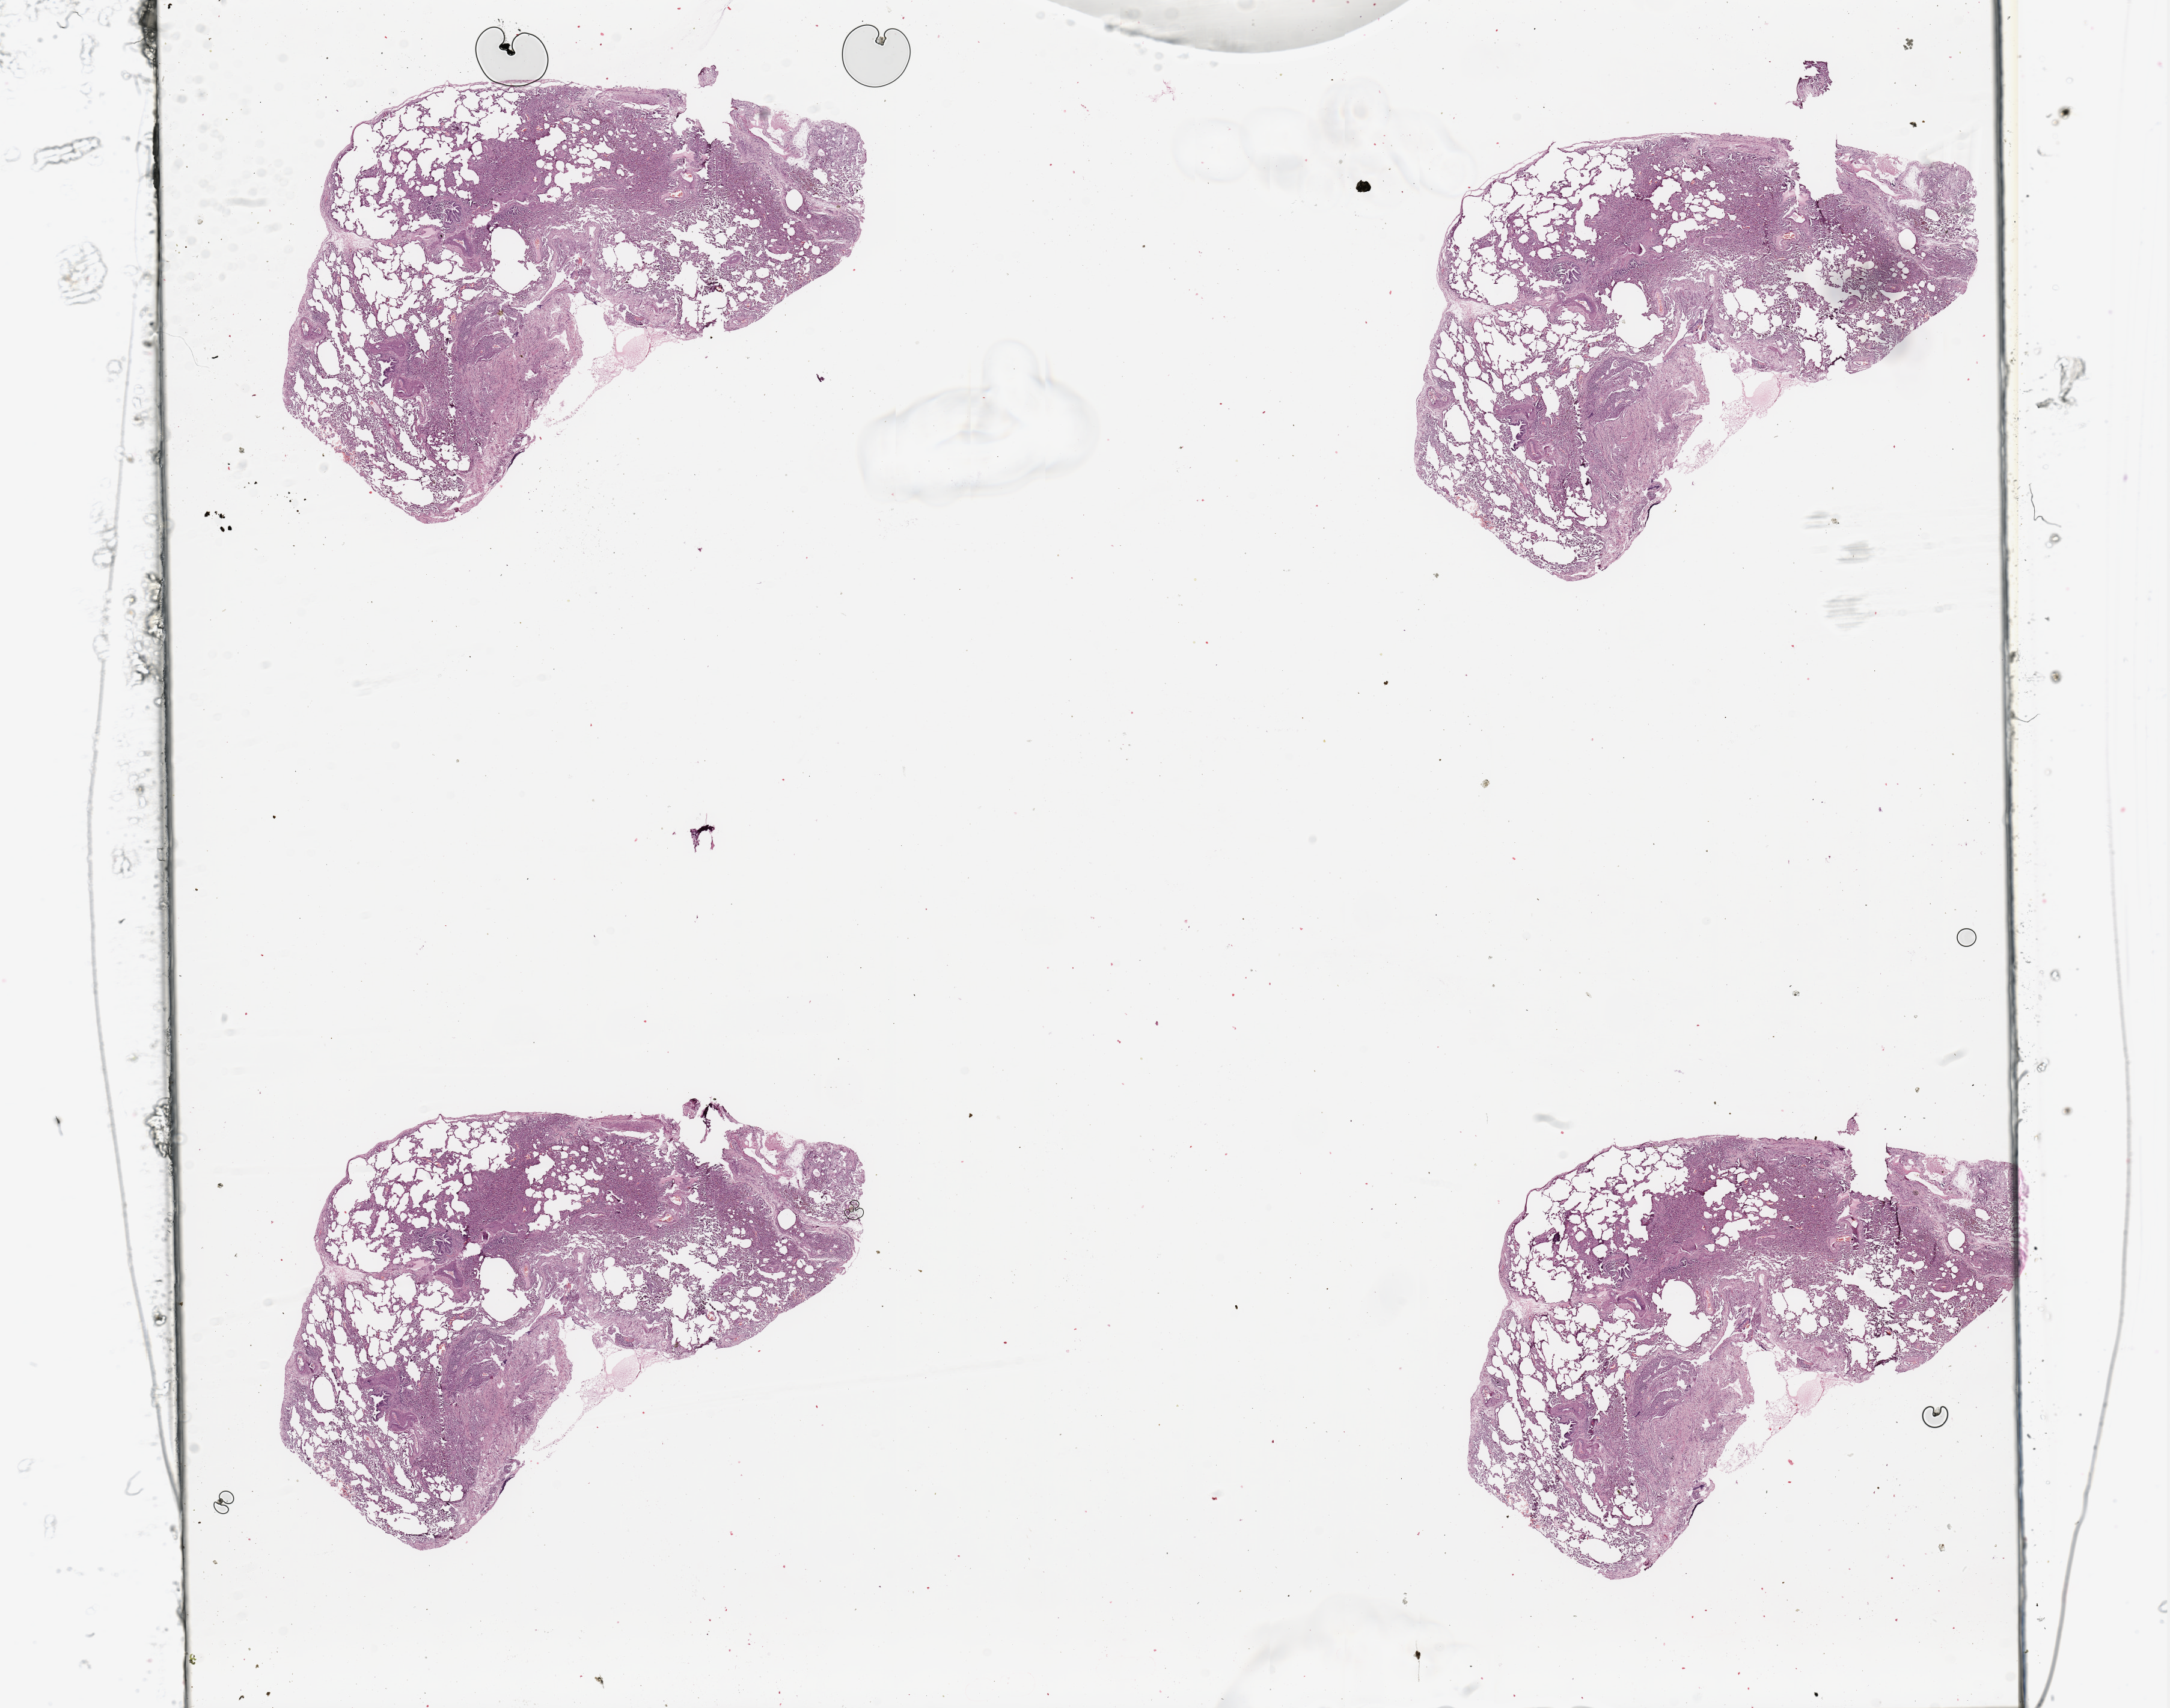
Whole-slide histology image, H&E, a low-resolution overview of the entire scanned area, about 28.5 x 22.5 mm (from a 20x scan), normal (non-tumour) tissue sample, sampled site: lung. 46-year-old male patient.
• this section: normal (non-tumour) tissue from the same patient
• patient diagnosis: Squamous cell carcinoma, NOS